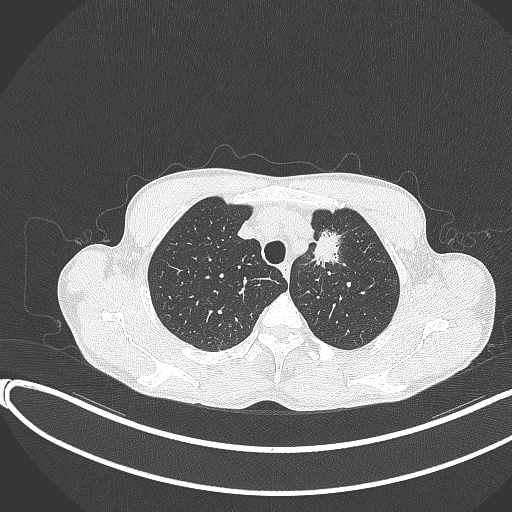
Chest CT, one axial slice; position 315 of 374 along the scan axis; reconstruction kernel B70f; 120 kVp; lung window (W 1500 / L -600 HU); 1 mm slice thickness; 512 × 512 image matrix, field of view 400 × 400 mm. Patient: male, 58 years. Case-level facts recorded for this patient, not image findings: clinical TNM (as recorded): T1c N1 M0.
Outlined on this slice (rectangle marked by the reading radiologist):
- lung tumour (recorded histology: adenocarcinoma): bounding box <313,224,358,271> (left, top, right, bottom; pixels)